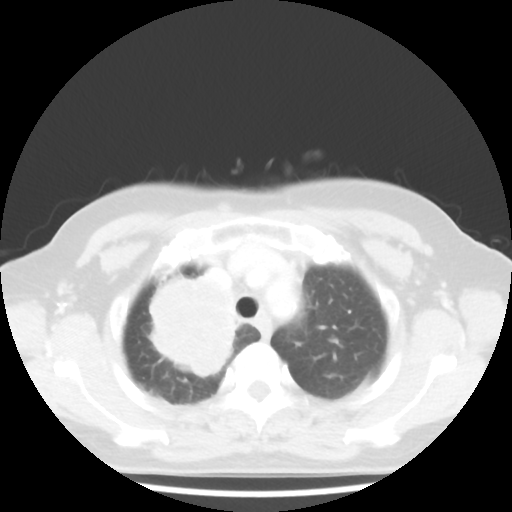
Chest CT, one axial slice. Position 36 of 44 along the scan axis. Lung window (W 1500 / L -600 HU). 5 mm slice thickness. 512 × 512 image matrix, field of view 316 × 316 mm. Female patient, age 62 years. Case-level facts recorded for this patient, not image findings: clinical TNM (as recorded): T3 N0 M0.
Structures marked on this image (bounding box drawn by a radiologist):
- lung tumour (recorded histology: small cell carcinoma): bounding box [x1, y1, x2, y2] px = [137, 265, 239, 383]